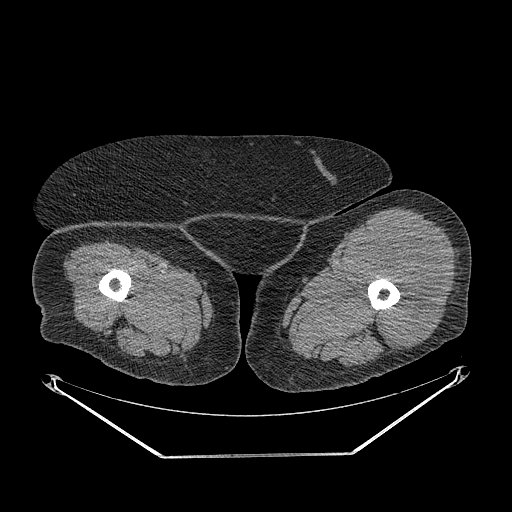
CT of an extremity soft-tissue mass (from a PET/CT study), one axial slice. Position 241 of 267 along the scan axis. Reconstruction kernel STANDARD. 140 kVp. Soft-tissue window (W 400 / L 40 HU). 3.75 mm slice thickness. 512 × 512 image matrix, field of view 500 × 500 mm. Female patient. From the clinical record (not read from this slice): histological type: undifferentiated – high grade; grade: high; site of the primary tumour: left thigh.
Outlined on this slice (expert contour drawn on MRI and transferred to this co-registered scan by the dataset authors):
- gross tumour volume including surrounding oedema: bounding box (x1, y1, x2, y2) in pixels: (352, 226, 442, 350)
- gross tumour volume (mass): (354, 226, 442, 350)